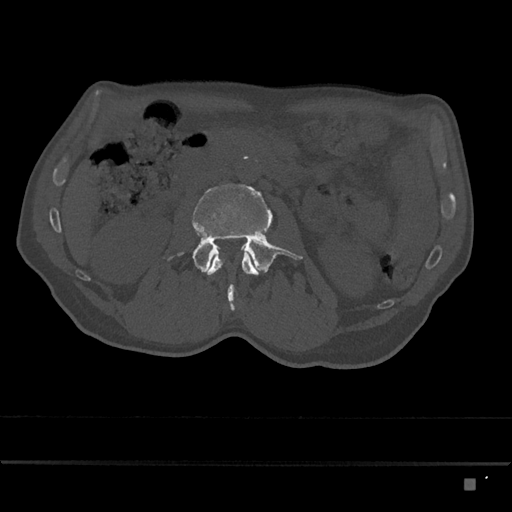
CT including the spine, one axial slice. 120 kVp. Bone window (W 1800 / L 400 HU). 0.5 mm slice thickness. 512 × 512 image matrix, field of view 390 × 390 mm. Male patient, age 72 years. Case-level facts recorded for this patient, not image findings: primary cancer: prostate.
Structures marked on this image (semi-automatically segmented with operator editing):
- L2 vertebra: bounding box (x1, y1, x2, y2) in pixels: (205, 252, 259, 311)
- L3 vertebra: (168, 184, 303, 274)